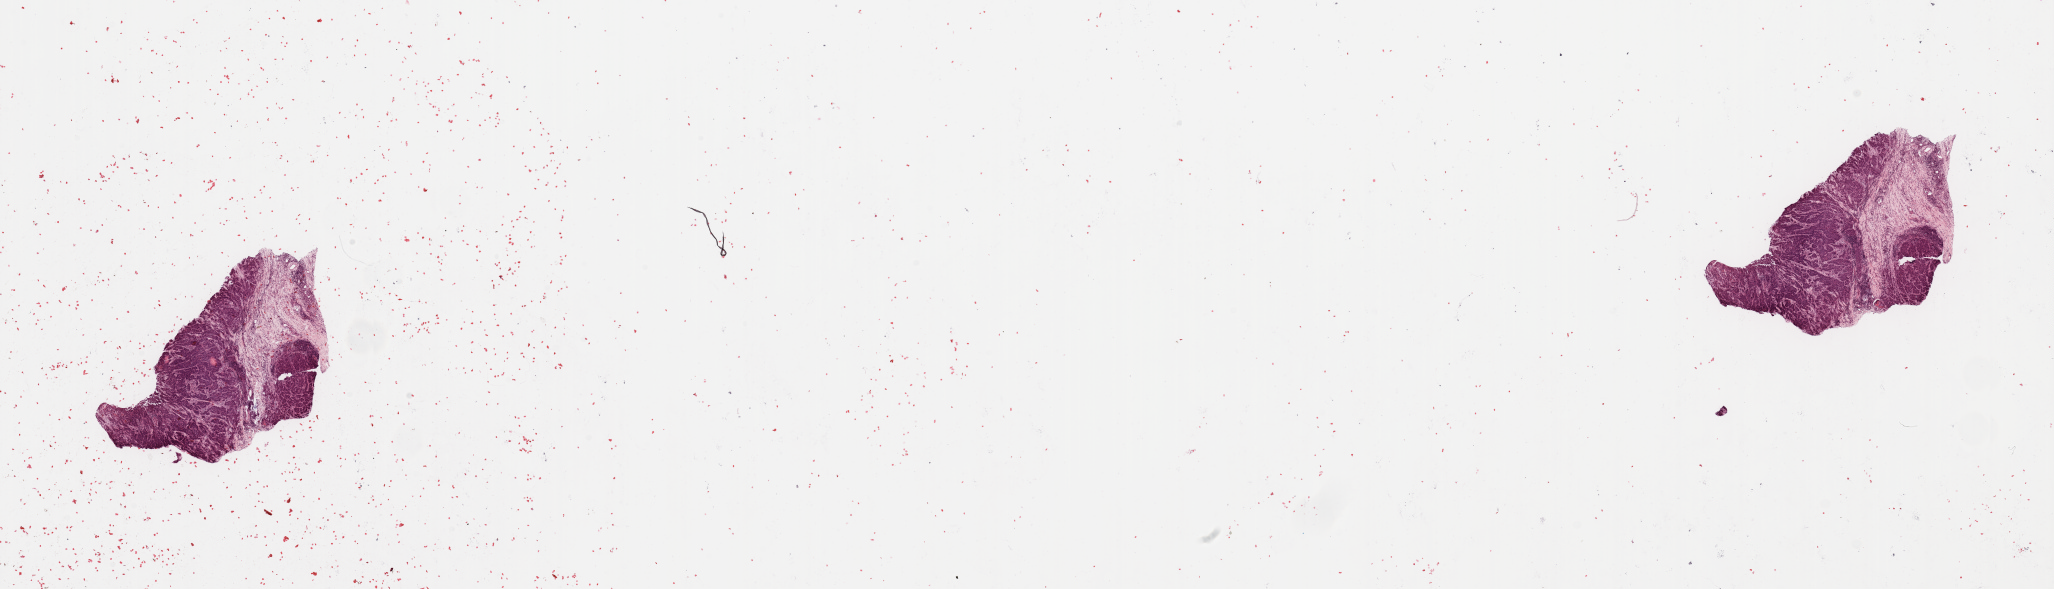
Whole-slide histology image, Hematoxylin and eosin (H&E) stained — a low-resolution overview of the entire scanned area, about 32.5 x 9.3 mm (slide scanned at 20x); tumour tissue sample, sampled site: larynx. Patient: male, age 62 years. Histologic grade: G2 (moderately differentiated). Slide review estimates, as recorded: tumour nuclei 85%, necrosis 2%.
• diagnosis: Squamous cell carcinoma, NOS (larynx, NOS)
• AJCC pathologic stage: III
• primary tumour site (as recorded): larynx